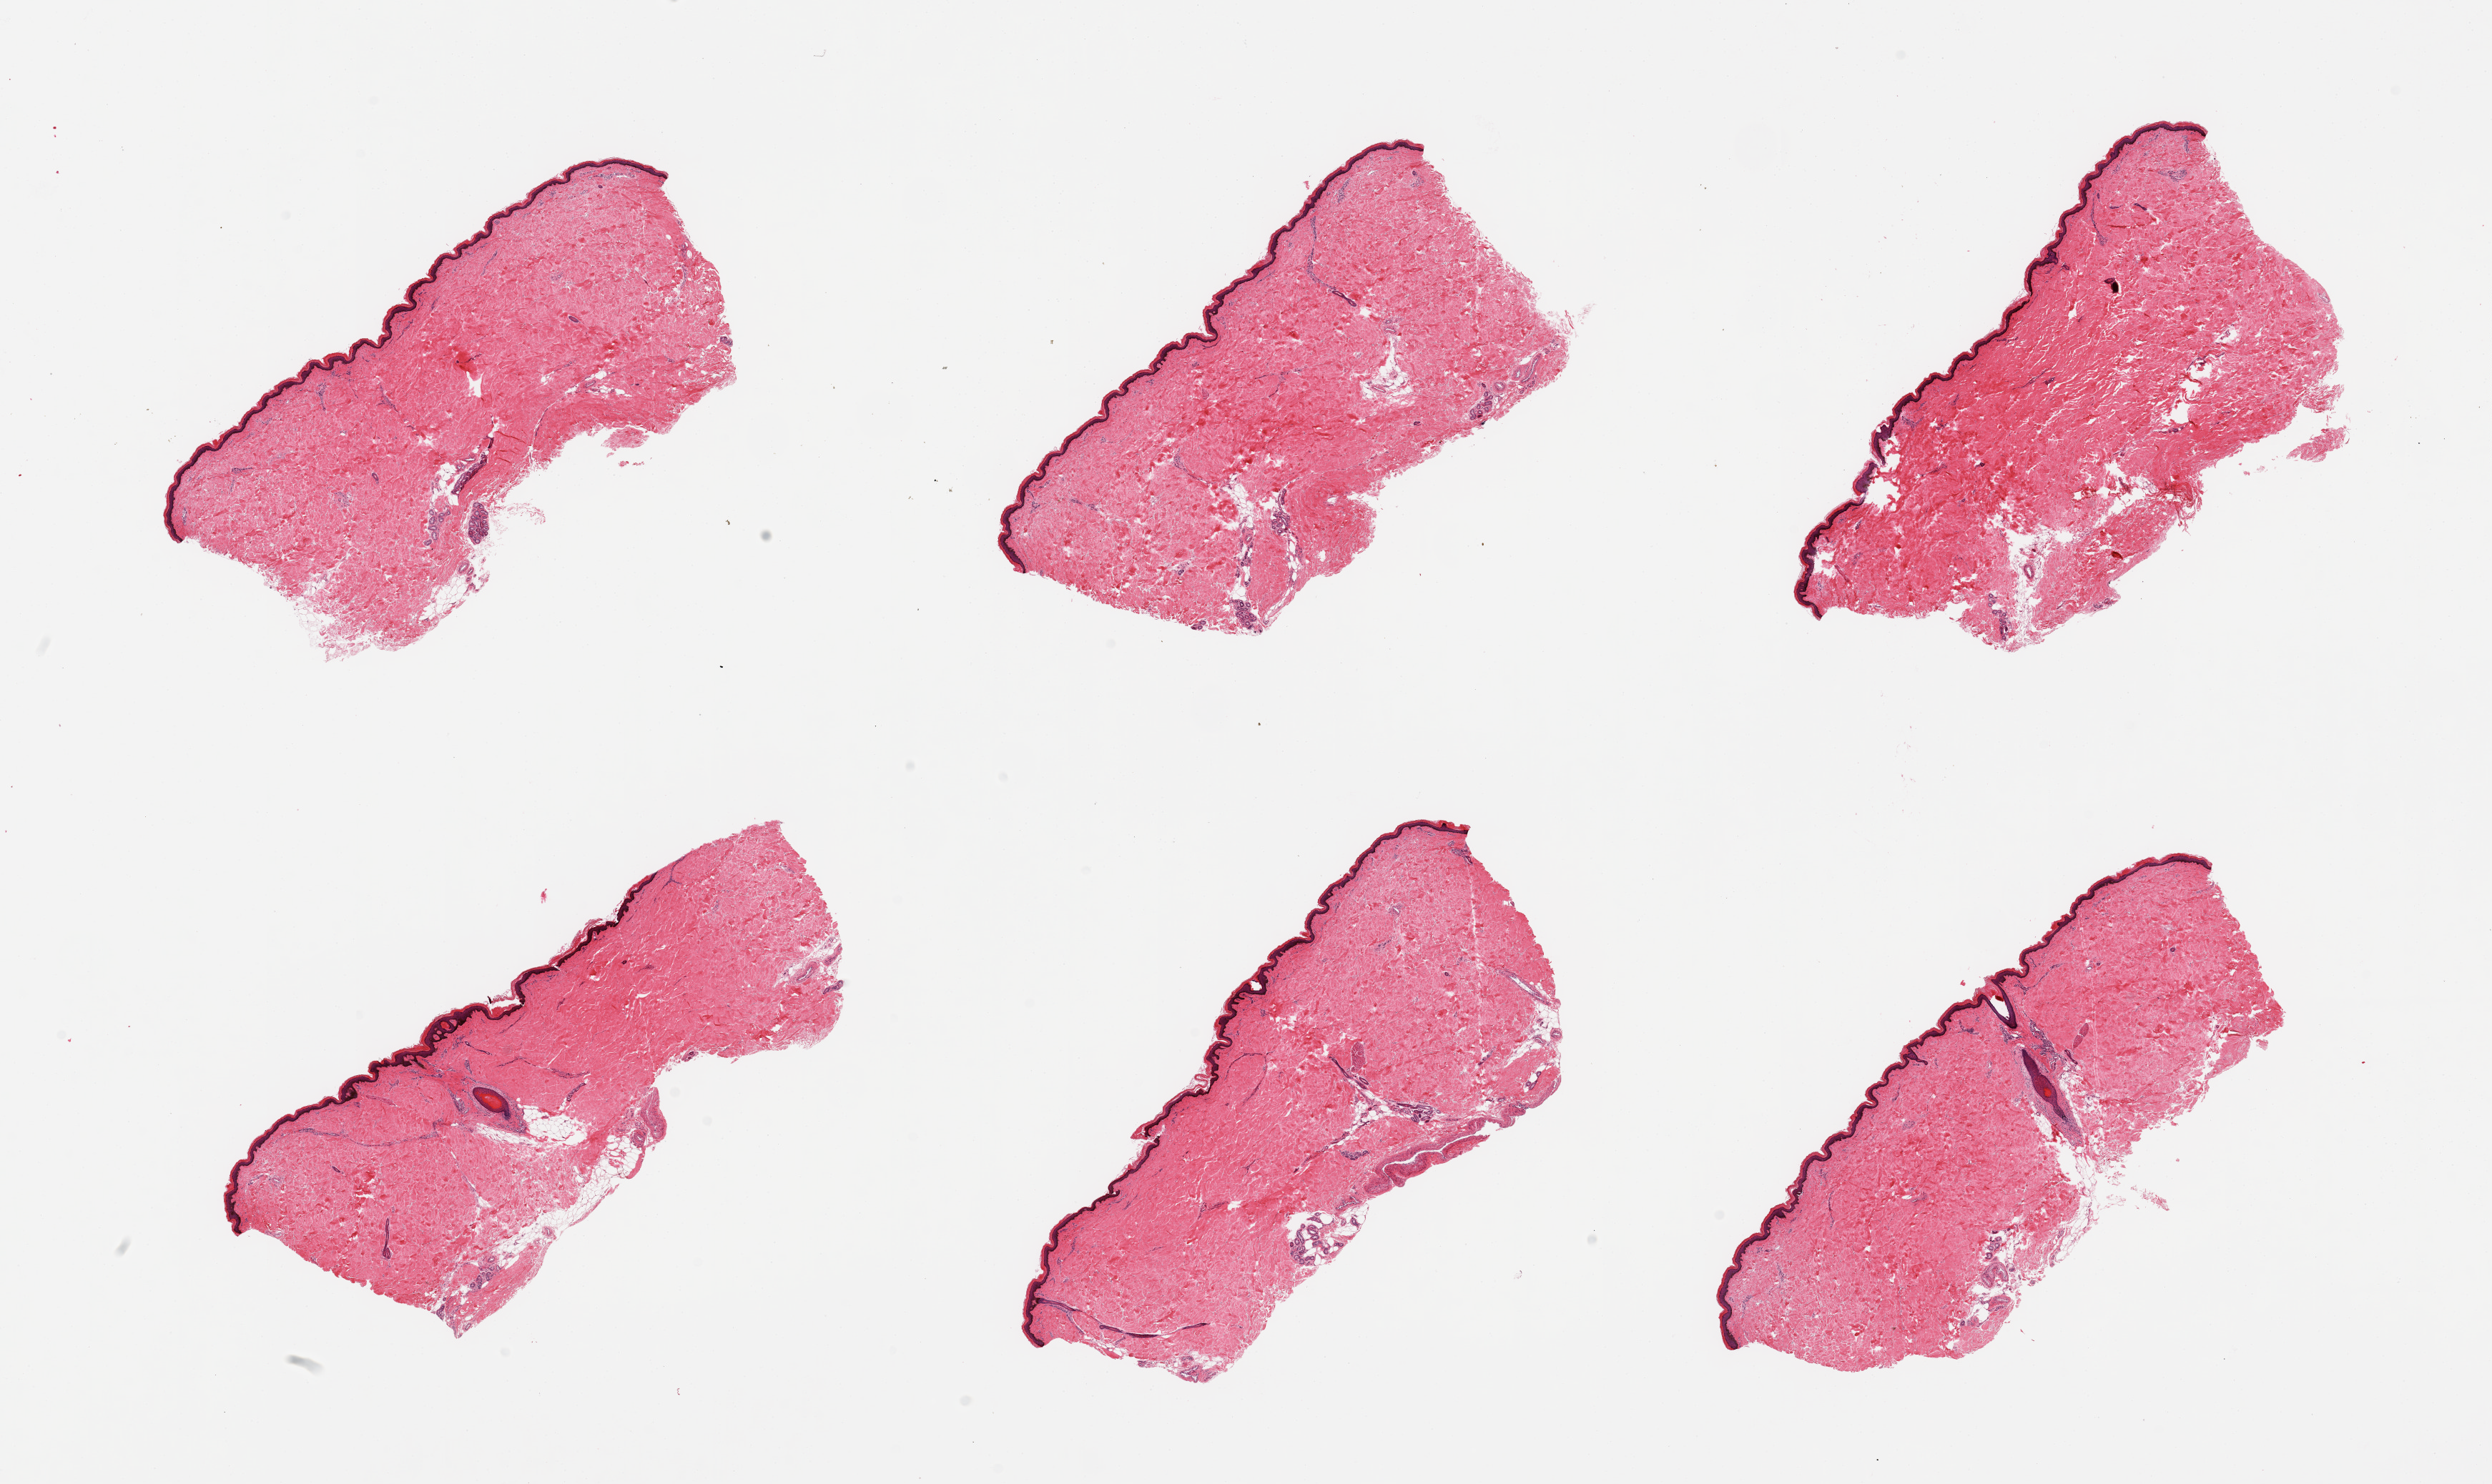
Whole-slide image, H&E stain, brightfield, shown as a low-resolution overview of the whole scanned area (about 27.6 x 16.4 mm), PAXgene-fixed, paraffin-embedded tissue, sampled site (target tissue): skin of lower leg, tissue donor sample. Donor: male.
Reviewer comment on this tissue sample: 6 pieces; well trimmed; 5% intradermal fat.